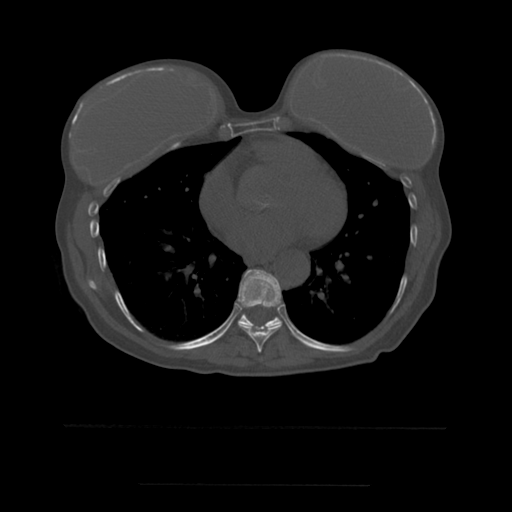
CT including the spine, one axial slice; position 332 of 544 along the scan axis; bone window (W 1800 / L 400 HU); 1.25 mm slice thickness; 512 × 512 image matrix, field of view 350 × 350 mm. Patient age 58 years. From the clinical record (not read from this slice): primary cancer: lung.
Structures marked on this image (semi-automatic segmentation, software-assisted and operator-edited):
- T8 vertebra: bounding box <238,270,283,353> (left, top, right, bottom; pixels)
- T9 vertebra: <215,302,281,341>